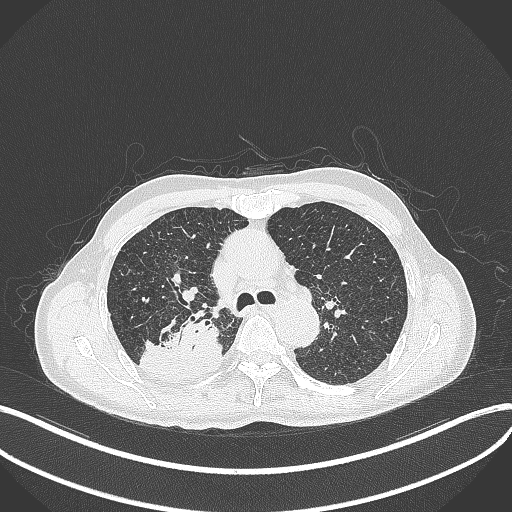
Chest CT, one axial slice; slice 306 of 428 in the series (ordered by position); 120 kVp; lung window (W 1500 / L -600 HU); 512 × 512 image matrix, field of view 400 × 400 mm. Male patient, age 79 years. From the clinical record (not read from this slice): clinical TNM (as recorded): T3 N0 M0.
Structures marked on this image (rectangle marked by the reading radiologist):
- lung tumour (recorded histology: adenocarcinoma): box from (x=137, y=313) to (x=224, y=380) px